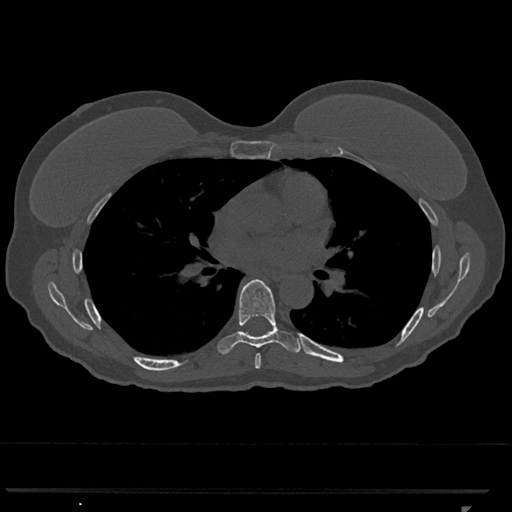
CT including the spine, one axial slice. Slice 718 of 793 in the series (ordered by position). Bone window (W 1800 / L 400 HU). 0.5 mm slice thickness. 512 × 512 image matrix. Patient: female, 62 years. From the clinical record (not read from this slice): primary cancer: renal.
Annotated regions visible in this slice (semi-automatically segmented with operator editing):
- T6 vertebra: bounding box [x1, y1, x2, y2] px = [254, 354, 261, 369]
- T7 vertebra: [217, 279, 301, 354]